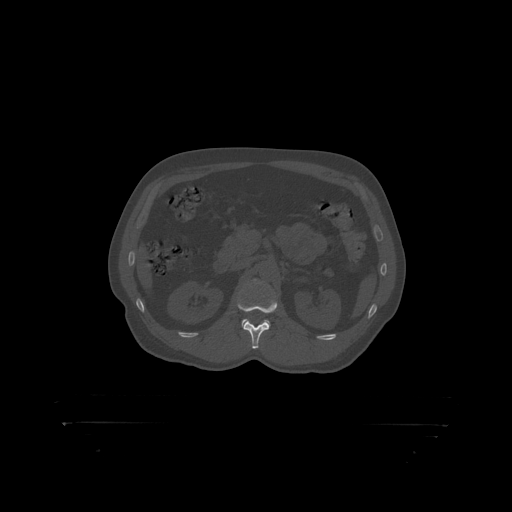
CT including the spine, one axial slice. Position 315 of 399 along the scan axis. Bone window (W 1800 / L 400 HU). 1.25 mm slice thickness. 512 × 512 image matrix. Patient: male, 46 years. From the clinical record (not read from this slice): primary cancer: skin.
Annotated regions visible in this slice (semi-automatically segmented with operator editing):
- L1 vertebra: box from (x=238, y=301) to (x=277, y=314) px
- L2 vertebra: (x=253, y=280)–(x=261, y=282)